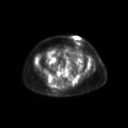
FDG PET of an extremity soft-tissue mass (from a PET/CT study), one axial slice. Slice 80 of 267 in the series (ordered by position). 3.27 mm slice thickness. 128 × 128 image matrix, field of view 600 × 600 mm. Female patient, age 60 years. Case-level facts recorded for this patient, not image findings: histological type: spindle cell suggestive of myxofibrosarcoma; grade: intermediate; site of the primary tumour: right buttock.
Outlined on this slice (expert contour drawn on MRI and transferred to this co-registered scan by the dataset authors):
- gross tumour volume (mass): bounding box [x1, y1, x2, y2] px = [48, 83, 61, 92]